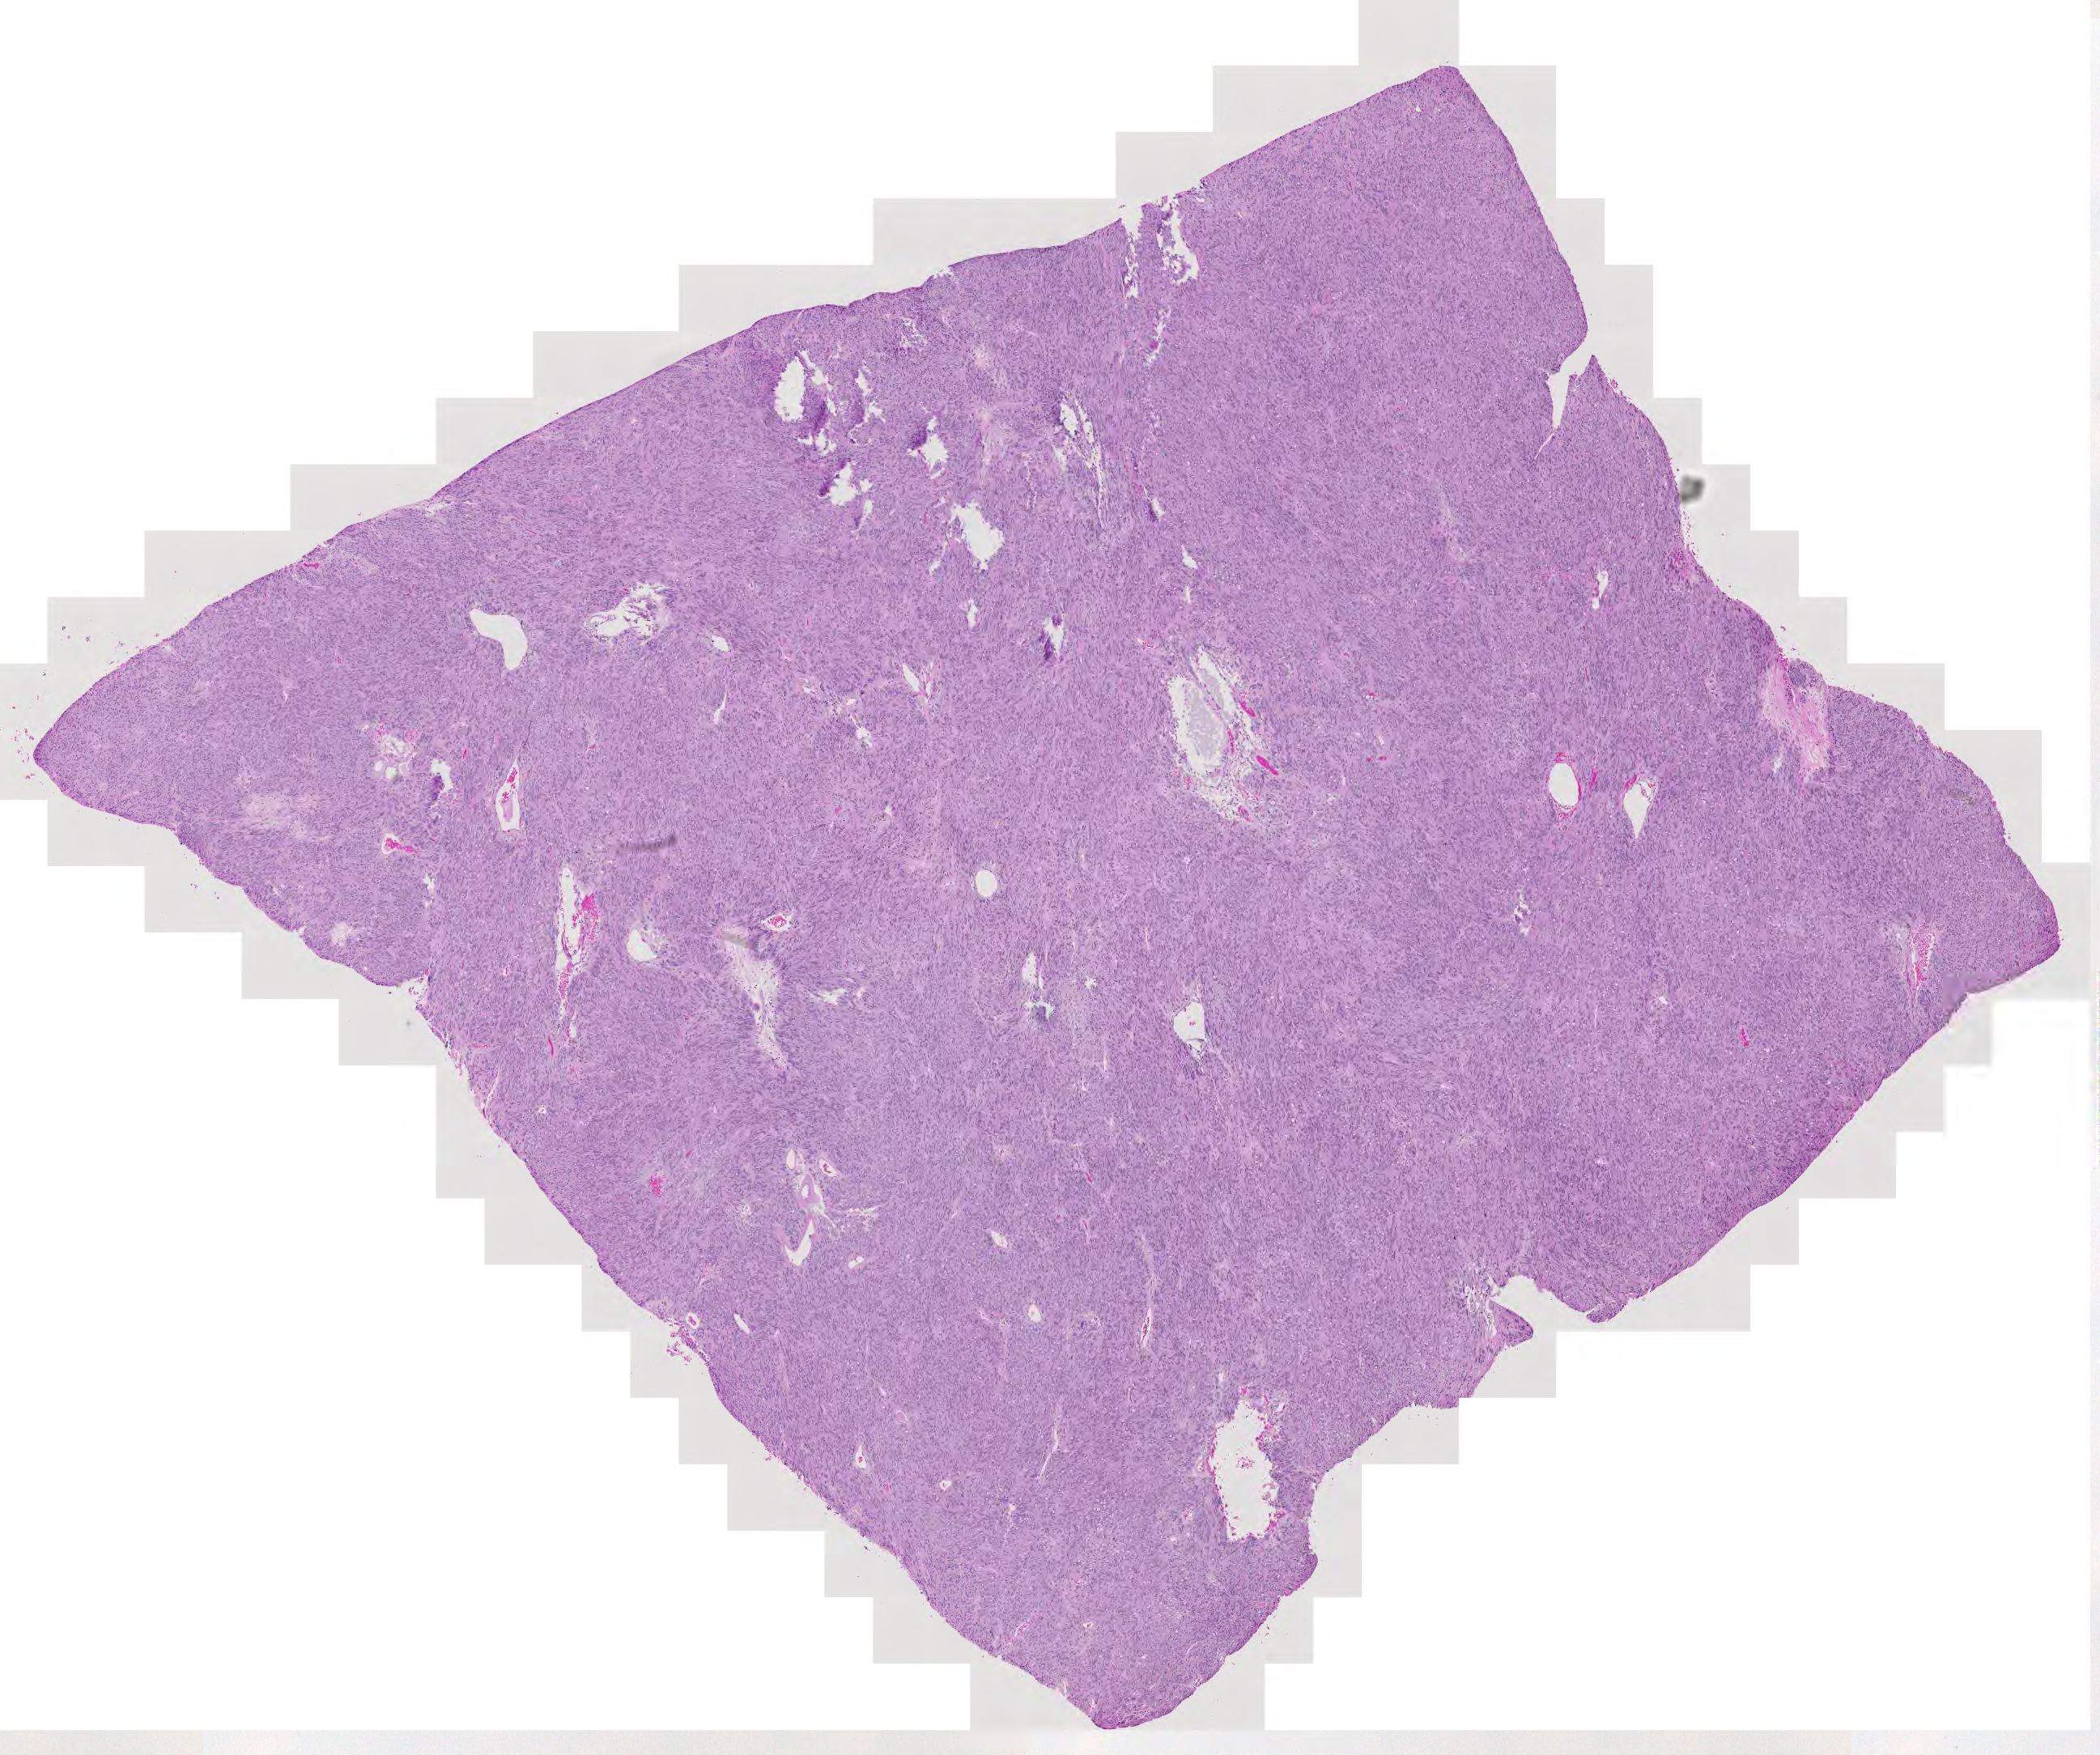
Whole-slide histology image, Hematoxylin and eosin (H&E) stained — whole scanned area (about 13.4 x 11.2 mm, acquisition: 20x scan) shown as a low-resolution overview. Male, 87 y/o.
* patient diagnosis (cohort enrolment): sarcoma (site not recorded at cohort level)